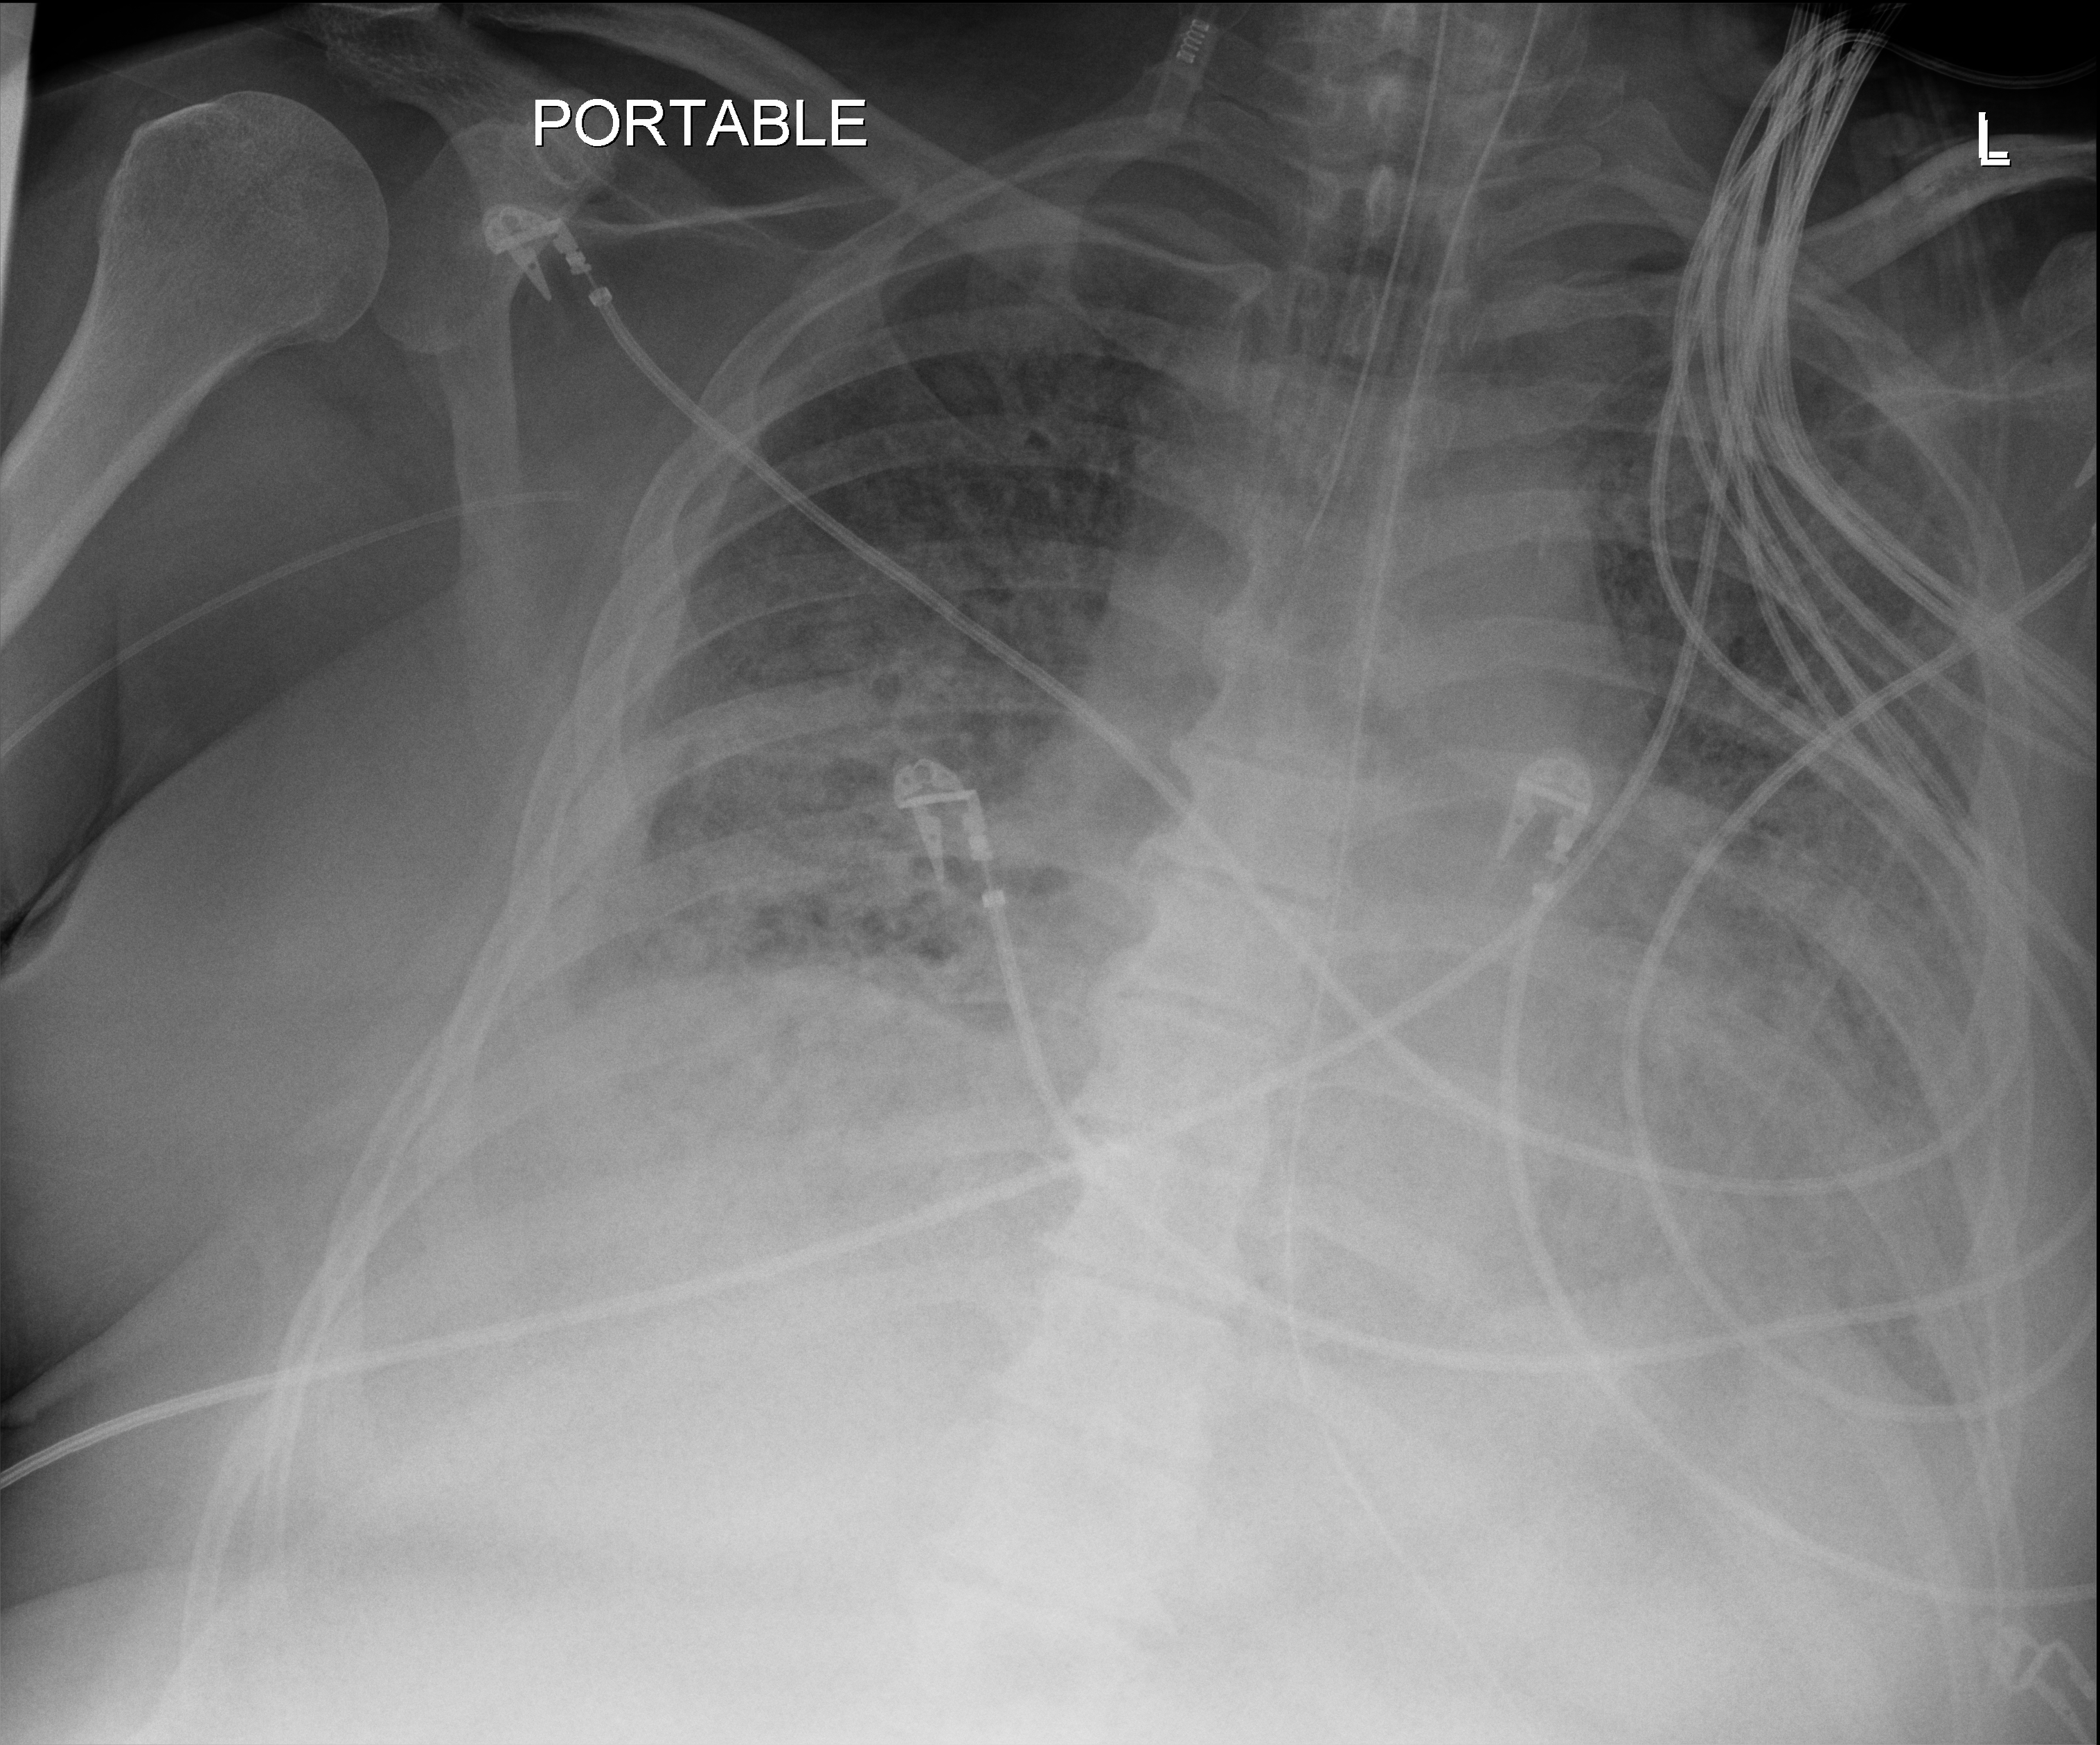
Chest X-ray (portable), anteroposterior (AP) projection. Patient hospitalised with COVID-19; male, aged 60–74 years.
Hospital-stay facts (about this admission, not read from this image; timing relative to this image not recorded):
- admitted to intensive care during this hospital stay: yes
- mechanically ventilated during this hospital stay: yes